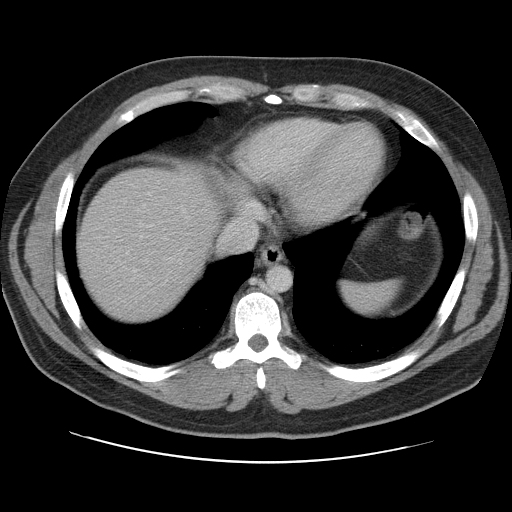
Contrast-enhanced abdominal CT, one axial slice. 120 kVp. Intravenous contrast given. Soft-tissue window (W 400 / L 40 HU). 512 × 512 image matrix. Male patient, age 35 years. From the clinical record (not read from this slice): diagnosis: colorectal cancer liver metastases, imaged before liver resection; multiple liver metastases: yes; largest metastasis: 2.8 cm; disease in both lobes: yes.
Outlined on this slice (outlined manually by an expert reader):
- hepatic veins: bounding box (x1, y1, x2, y2) in pixels: (133, 223, 255, 273)
- liver: (77, 168, 218, 322)
- planned liver remnant (the part of the liver to remain after resection): (77, 169, 218, 322)